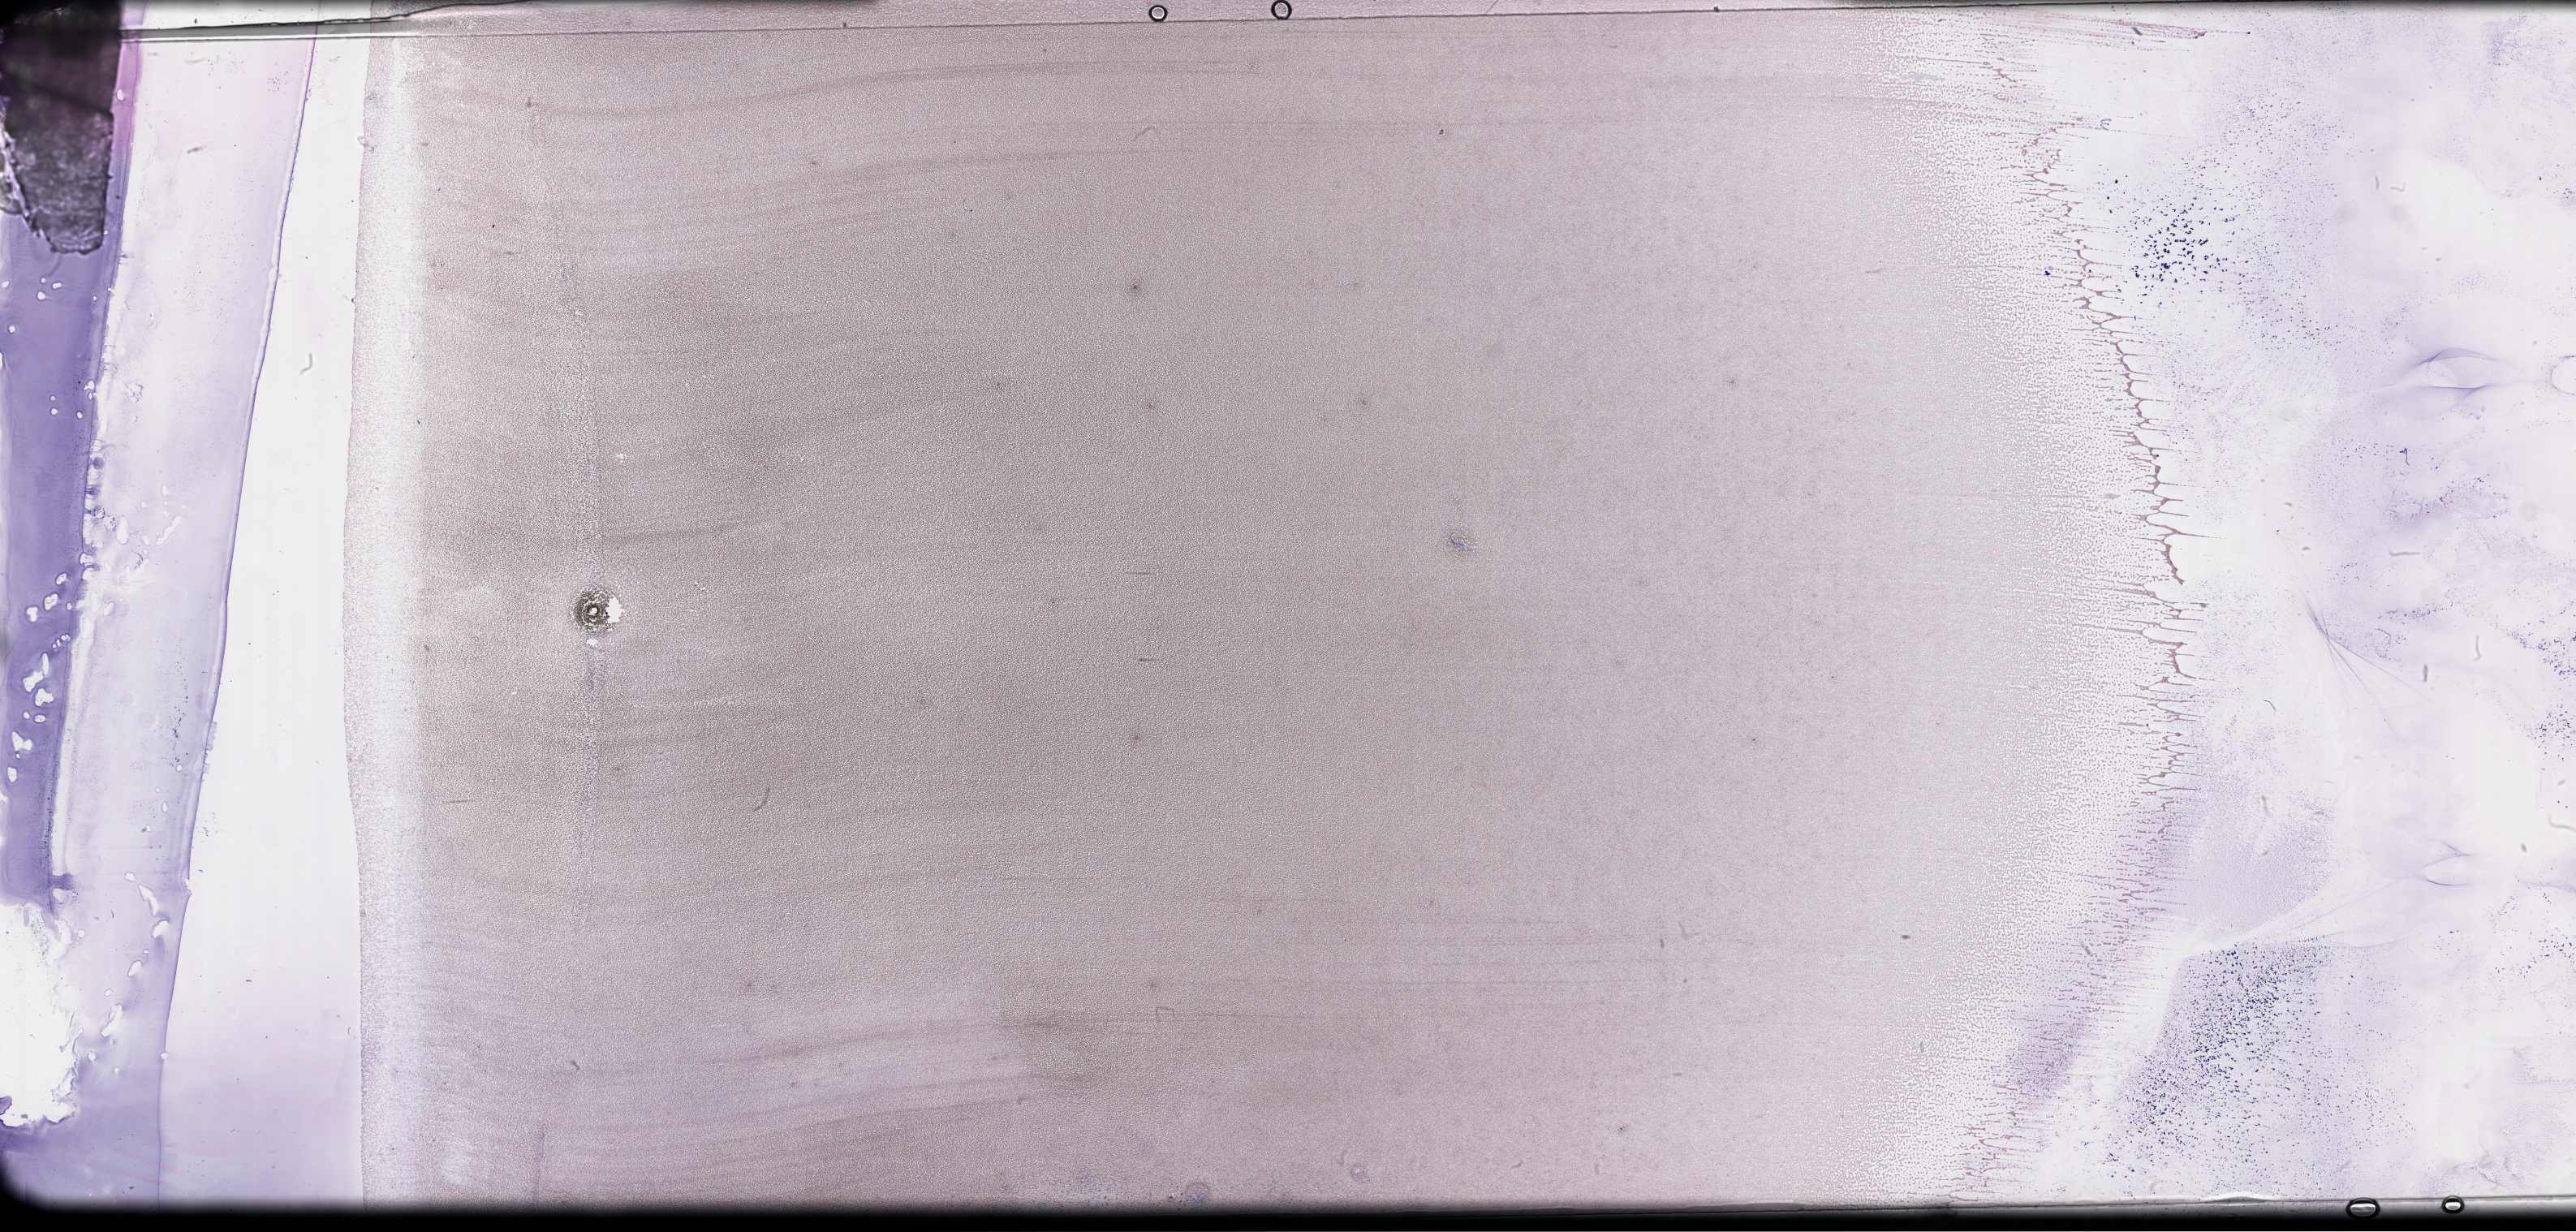
Wright-Giemsa-stained whole blood smear, whole-slide image, a low-resolution overview of the entire scanned area, about 51.3 x 24.5 mm. Smear from an EDTA sample. Collected on treatment. Patient: male.
• from a patient with: Plasma Cell Myeloma